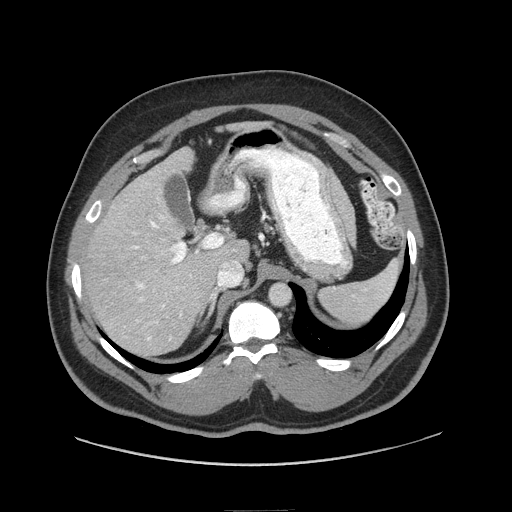
Contrast-enhanced abdominal CT (liver protocol), one axial slice; slice 50 of 87 in the series (ordered by position); 140 kVp; soft-tissue window (W 400 / L 40 HU); 2.5 mm slice thickness; 512 × 512 image matrix, field of view 440 × 440 mm. Case-level facts recorded for this patient, not image findings: diagnosis: hepatocellular carcinoma (patient treated with transarterial chemoembolisation; whether this scan precedes or follows treatment is not stated here); TNM stage (as recorded): Stage-II; Child-Pugh class: A.
Annotated regions visible in this slice (semi-automatically segmented with operator editing):
- liver parenchyma outside the tumour (the mass and vessels are separate outlines, so this box may not span the whole liver): bounding box (x1, y1, x2, y2) in pixels: (84, 148, 248, 356)
- liver vessels: (133, 215, 237, 340)